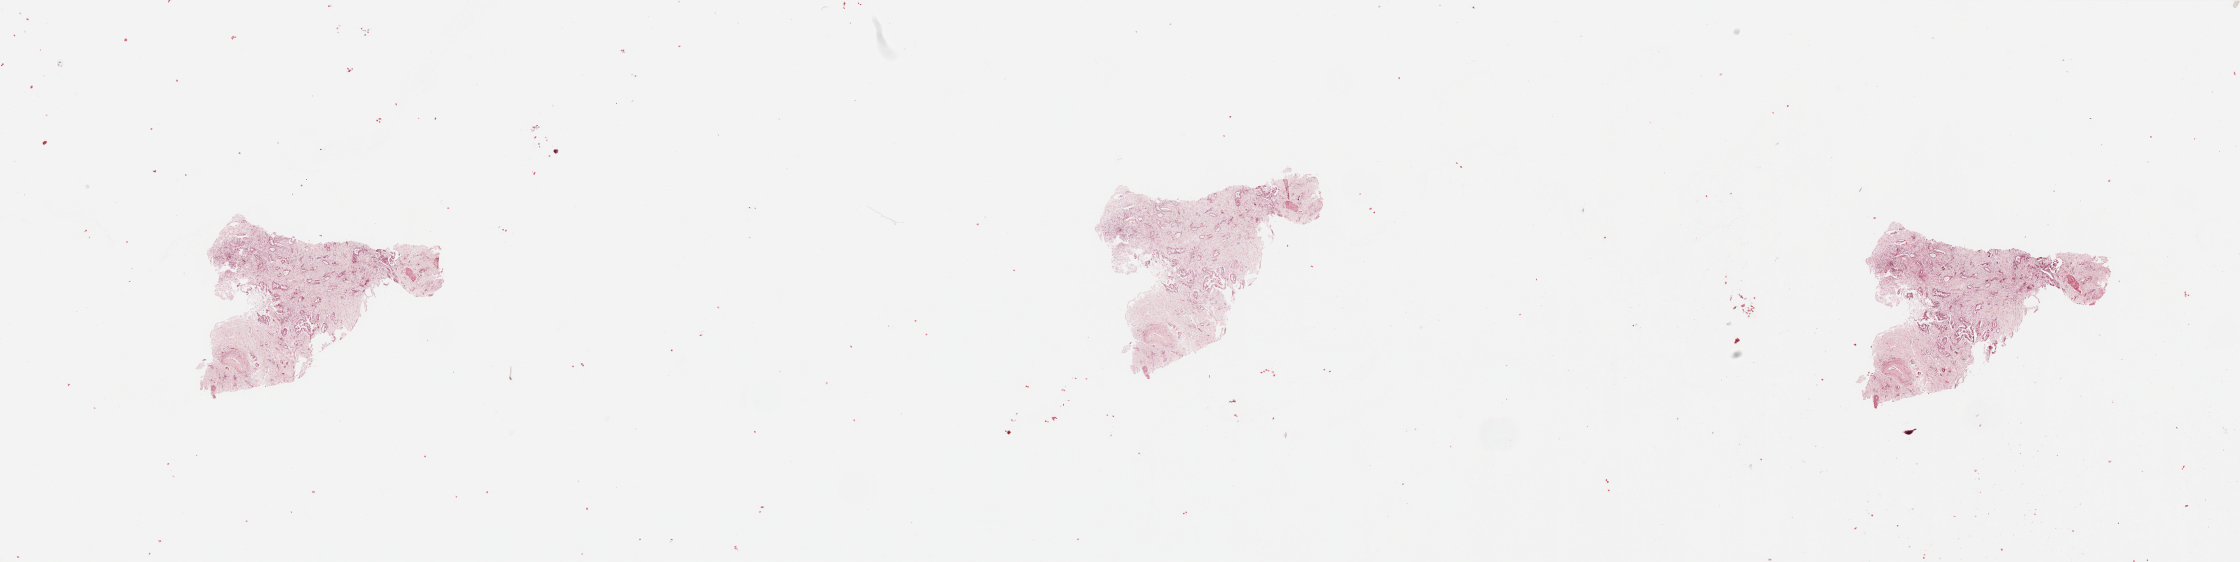
Digitized Hematoxylin and eosin (H&E) stained tissue section (whole slide) — low-resolution overview of the scanned area, about 35.4 x 8.9 mm; tumour tissue sample, sampled site: pancreas. Patient: male, age 59 years. Histologic grade: G2 (moderately differentiated). Pathologist review of this section (percent, as recorded): tumour nuclei 30%, necrosis 0%.
Histologic diagnosis: Infiltrating duct carcinoma, NOS. AJCC pathologic stage: III. Primary tumour site (as recorded): head.